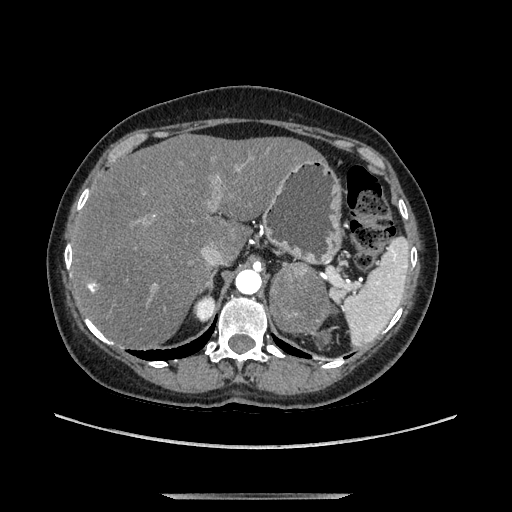
Contrast-enhanced abdominal CT, one axial slice; position 94 of 169 along the scan axis; soft-tissue window (W 400 / L 40 HU); 1.25 mm slice thickness; 512 × 512 image matrix, field of view 400 × 400 mm. Female patient. From the clinical record (not read from this slice): diagnosis: adrenocortical carcinoma; tumour side: left adrenal; tumour size at pathology: 9 cm; Ki-67 index: 2 %; stage (as recorded): 3.
Outlined on this slice (semi-automatic segmentation, software-assisted and operator-edited):
- mass: bounding box (x1, y1, x2, y2) in pixels: (272, 264, 330, 331)